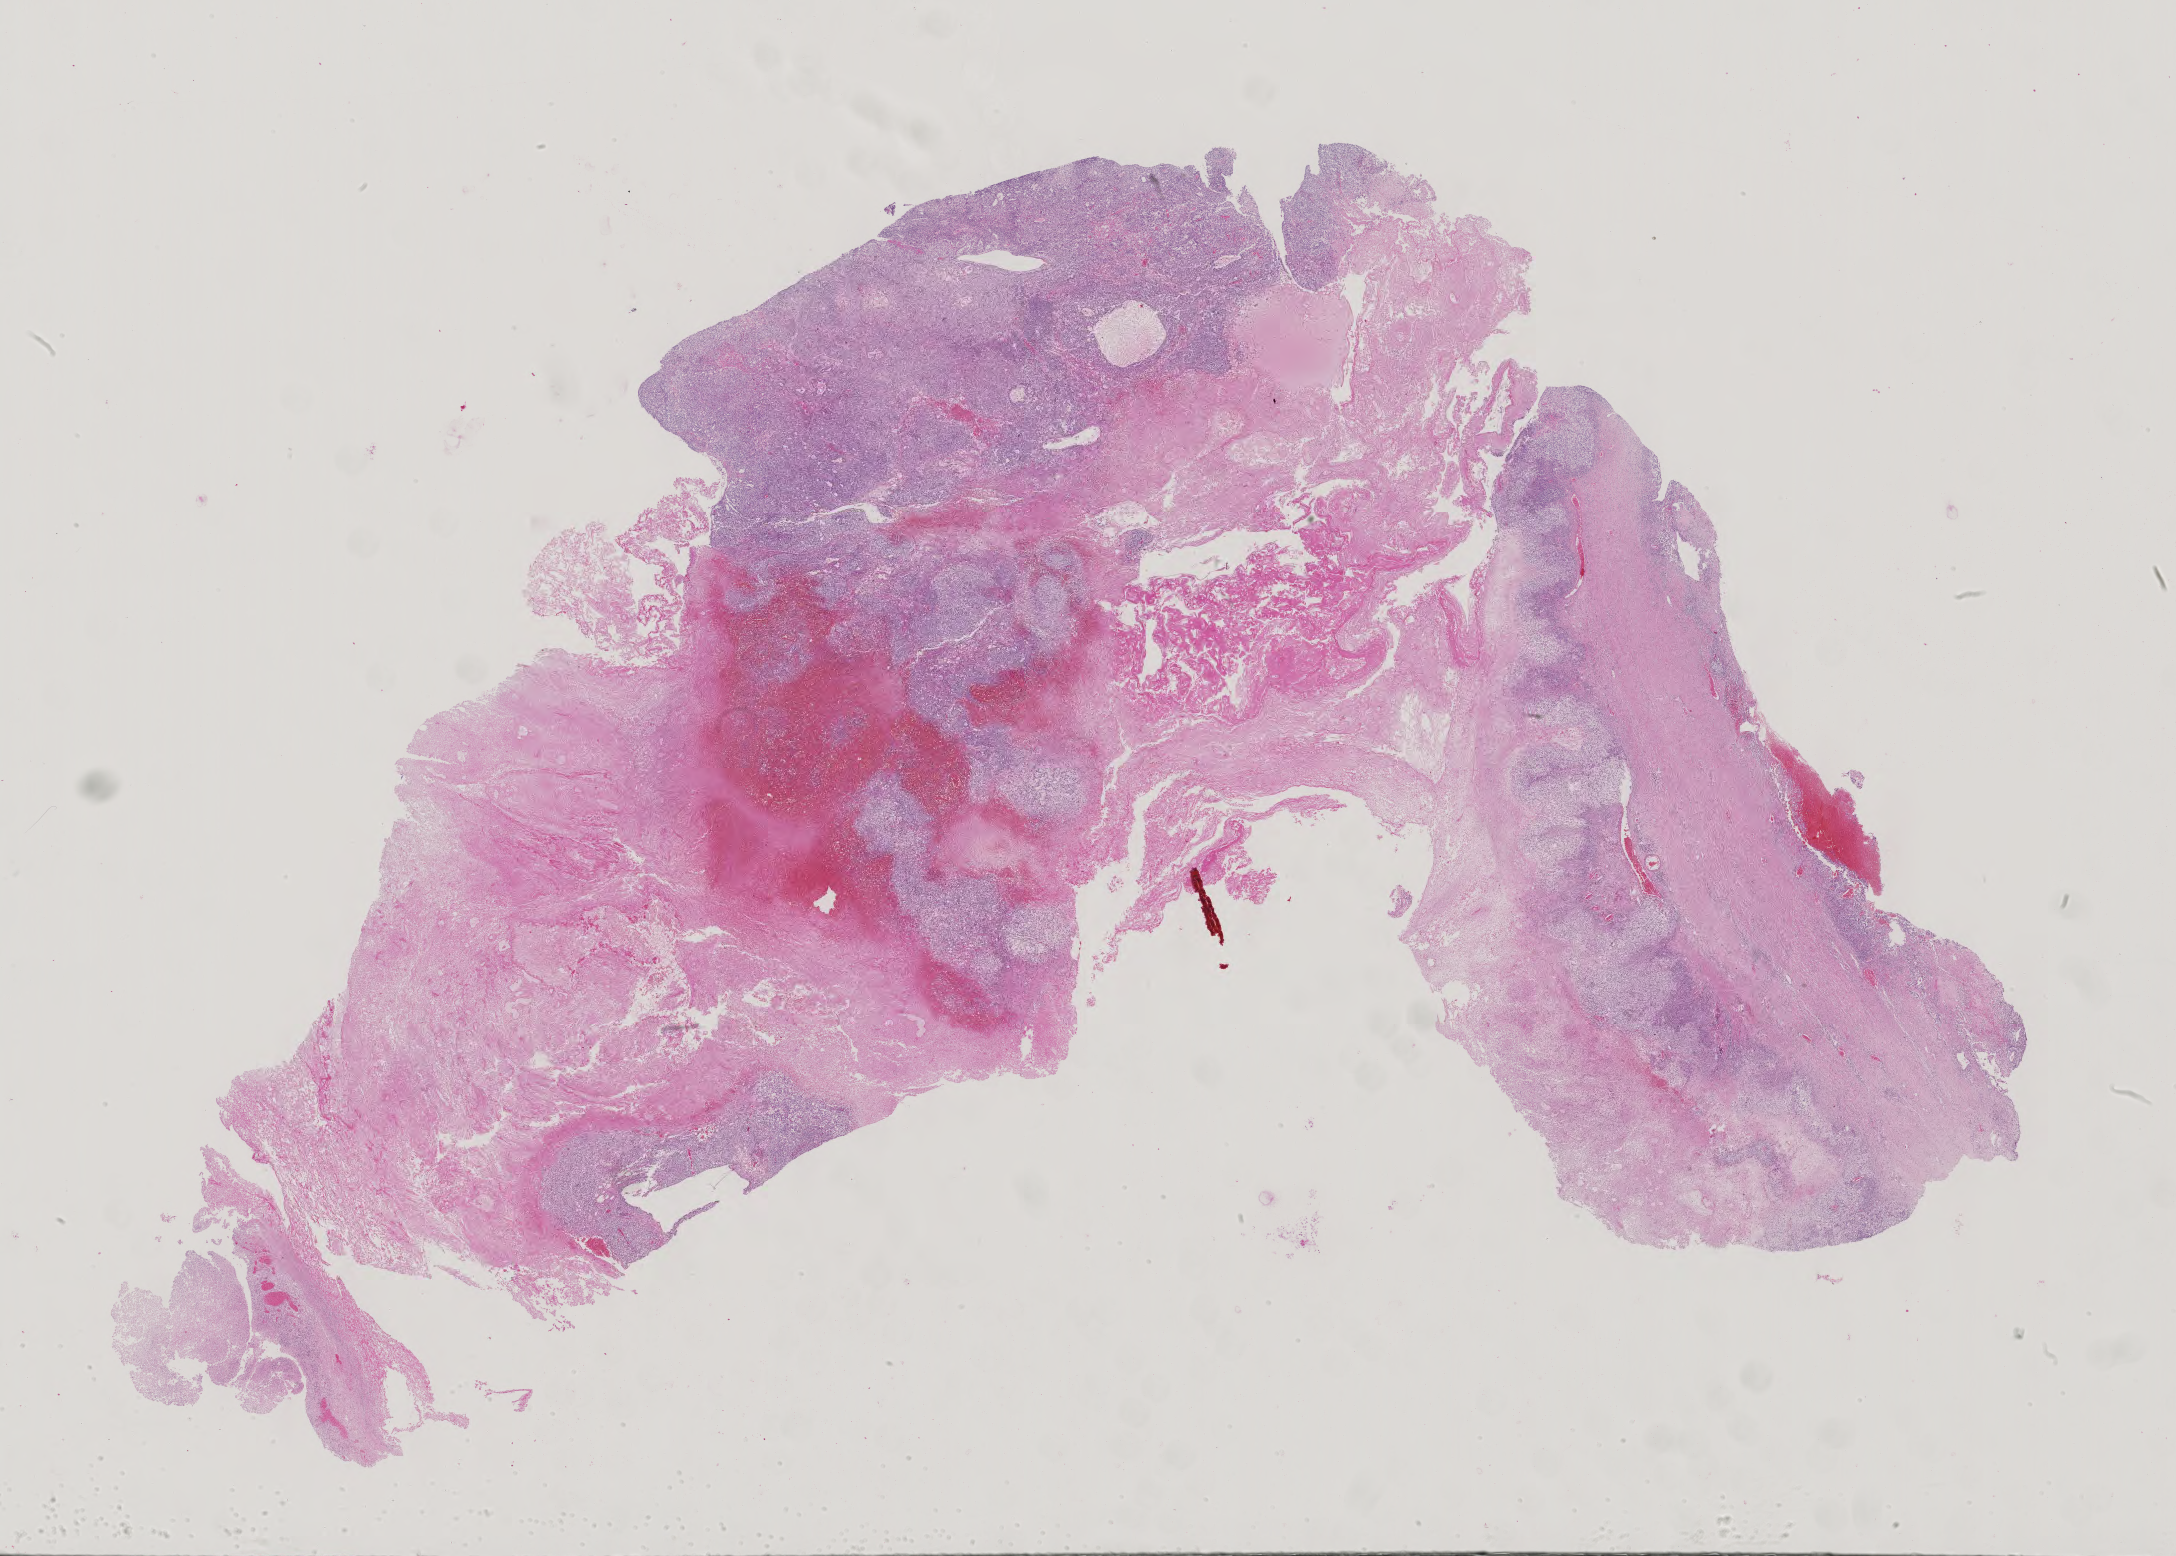
Whole-slide histology image, H&E — a low-resolution overview of the entire scanned area, about 31.7 x 22.7 mm (slide scanned at 40x). Patient sex: male.
Specimen: formalin-fixed paraffin-embedded (FFPE) diagnostic section; primary tumour sample from the testis.